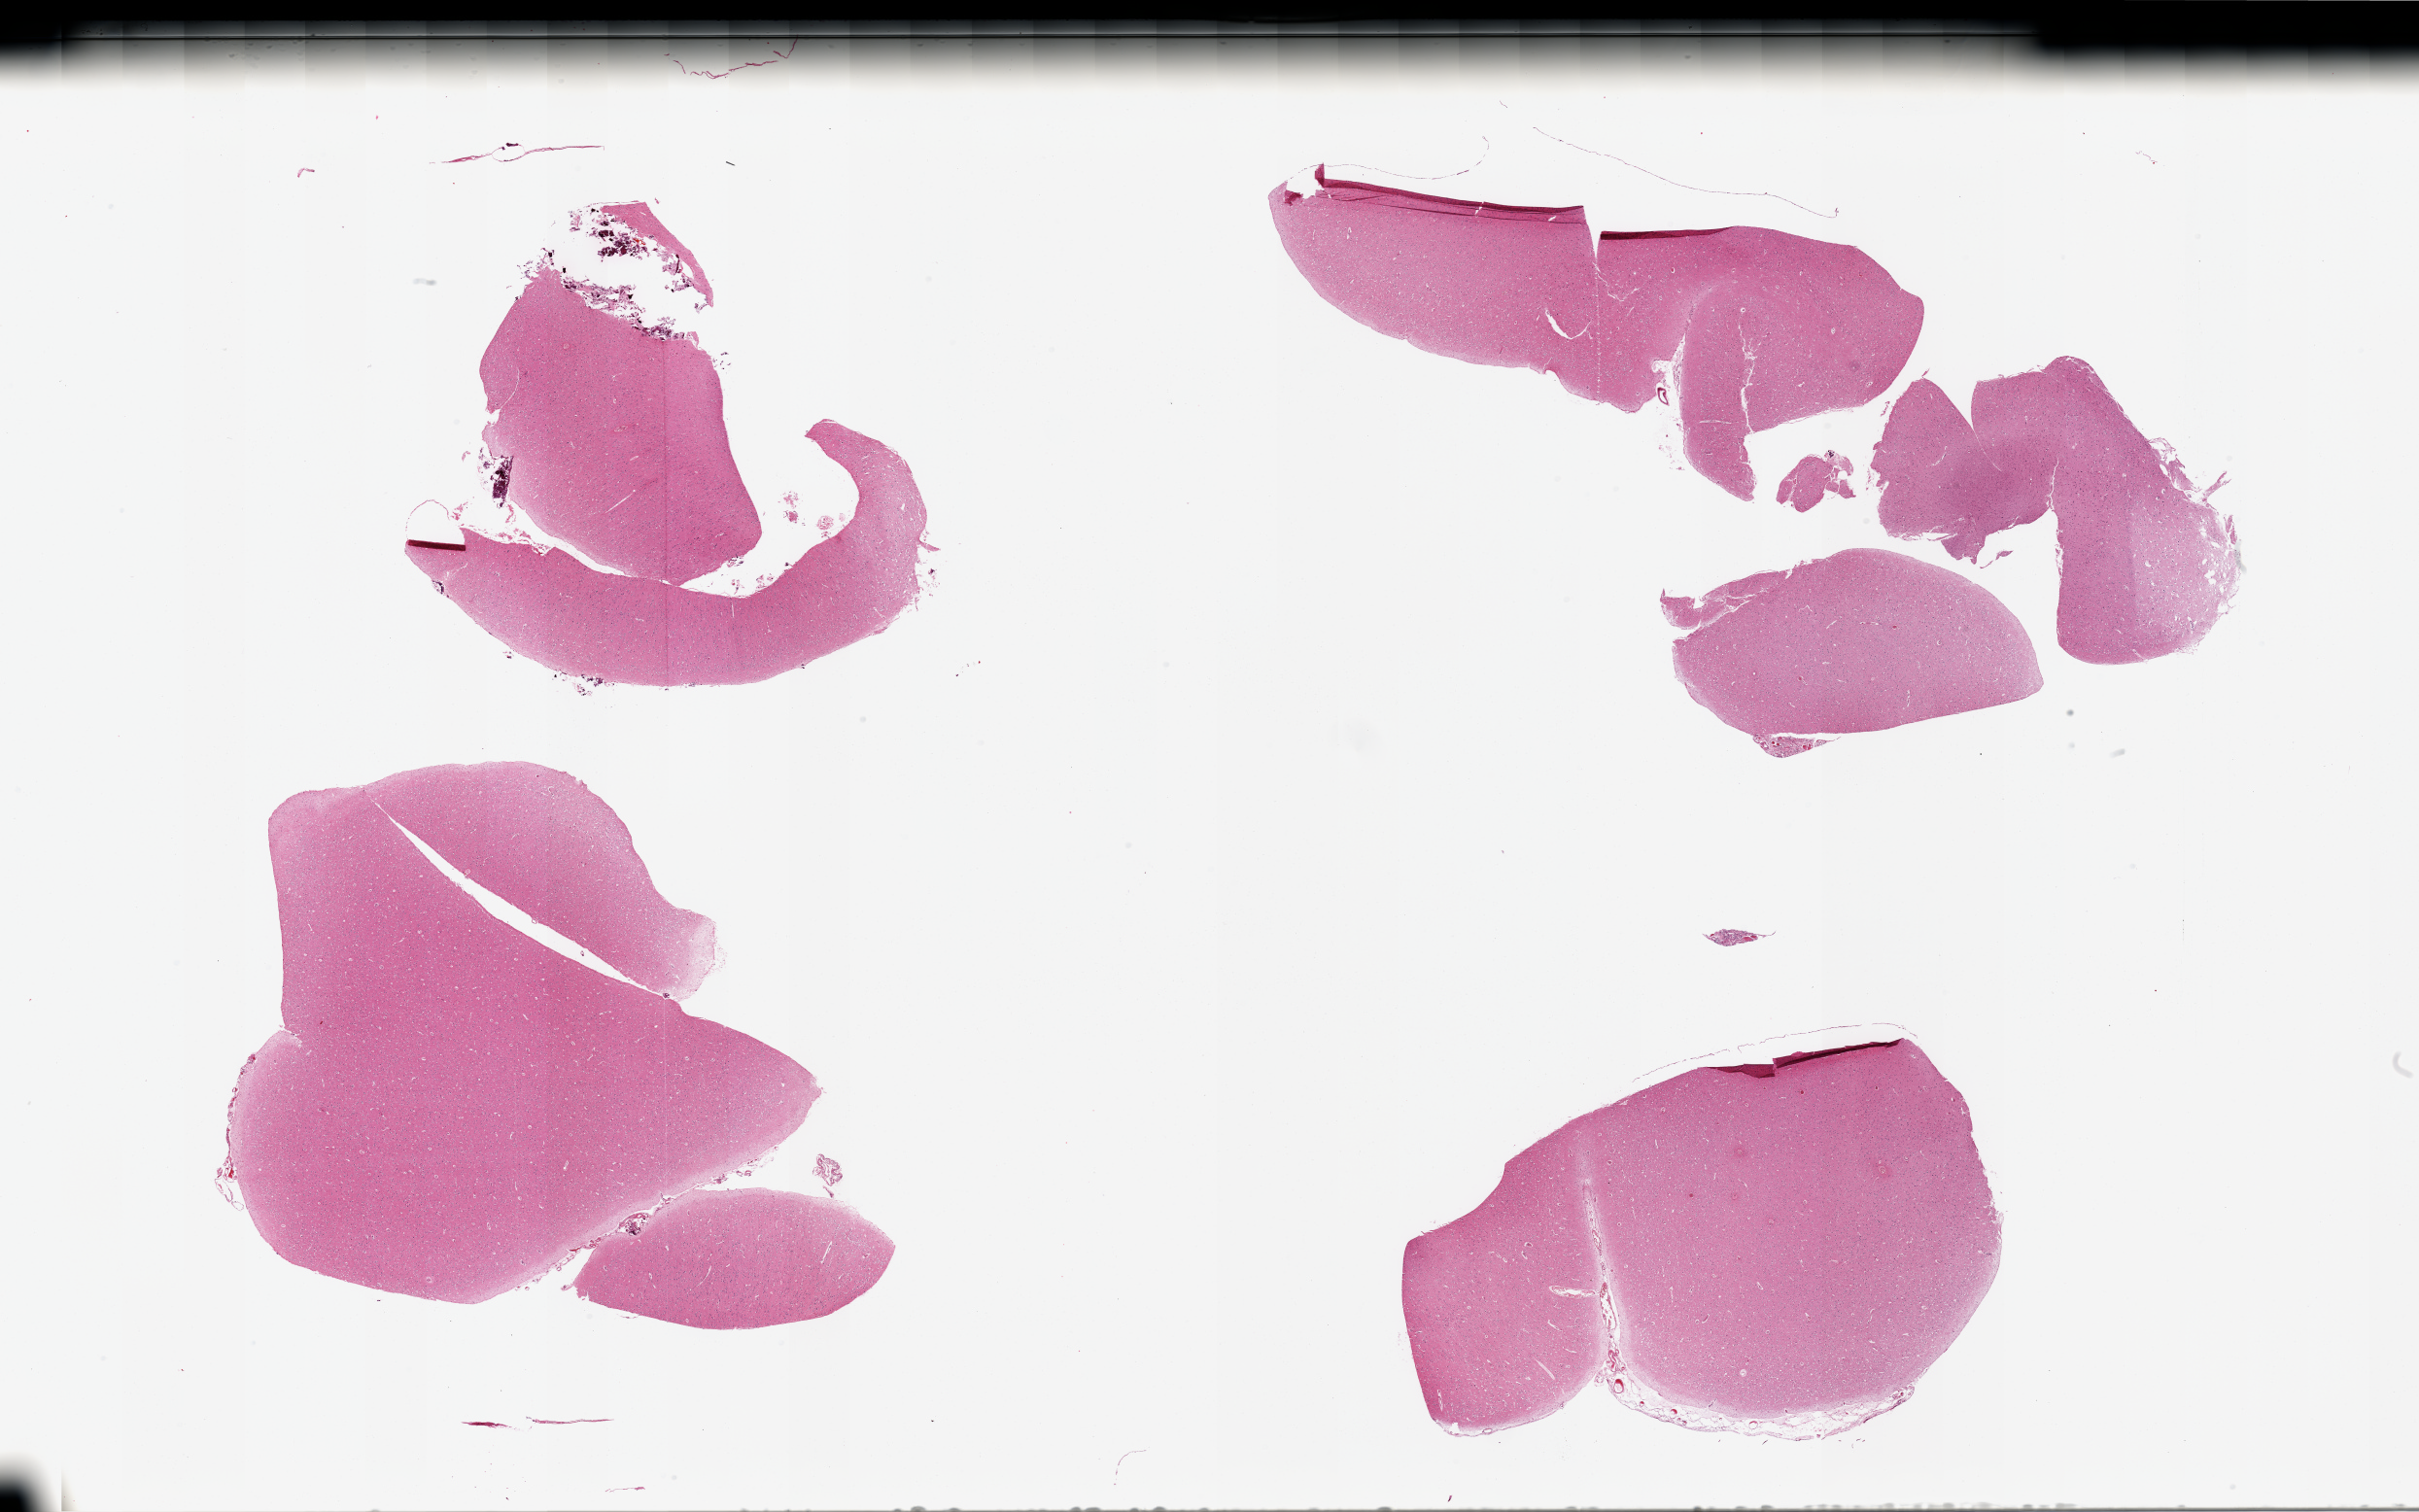
Haematoxylin and eosin whole-slide image, a low-resolution overview of the entire scanned area, about 39.4 x 24.6 mm; PAXgene-fixed, paraffin-embedded tissue; target tissue: cerebral cortex; donor tissue sample. Male donor.
Reviewer comment on this tissue sample: 4 fragmented pieces; tiny remnants of meninges with calcifications.